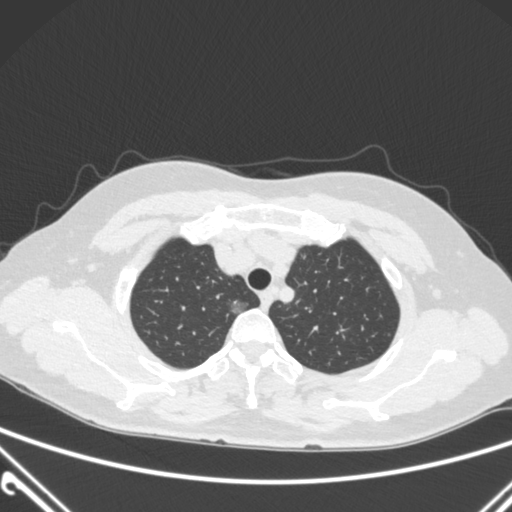
Chest CT, one axial slice. Position 237 of 300 along the scan axis. 120 kVp. Lung window (W 1500 / L -600 HU). 1 mm slice thickness. 512 × 512 image matrix, field of view 350 × 350 mm. Female patient, age 54 years. Case-level facts recorded for this patient, not image findings: clinical TNM (as recorded): T1a N0 M0; histopathological grade: G1.
Outlined on this slice (bounding box drawn by a radiologist):
- lung tumour (recorded histology: adenocarcinoma): bounding box [x1, y1, x2, y2] px = [228, 299, 254, 318]